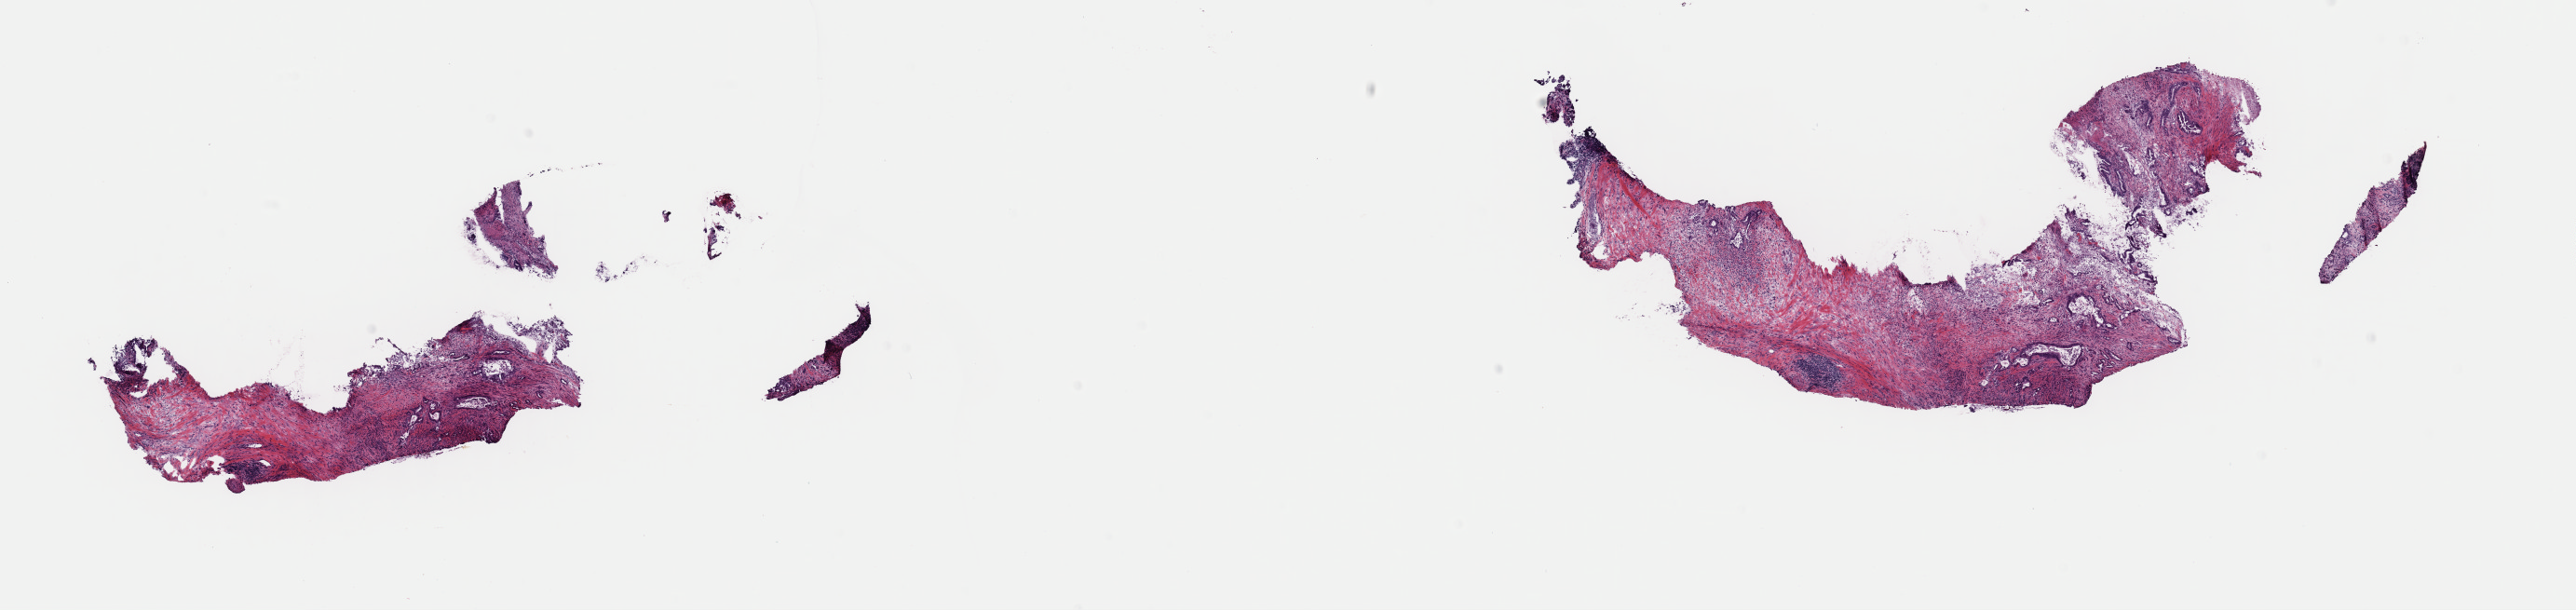
Digitized H&E tissue section (whole slide), shown as a low-resolution overview of the whole scanned area (about 21.9 x 5.2 mm, acquisition: 40x scan); frozen section from the top of the tissue portion; primary tumour sample from the pancreas. Female patient; age at initial diagnosis 79 years. Pathologist review of this section (percent, as recorded): tumour cells 40%, tumour nuclei 30%.
Histologic diagnosis: Adenocarcinoma, NOS (head of pancreas).